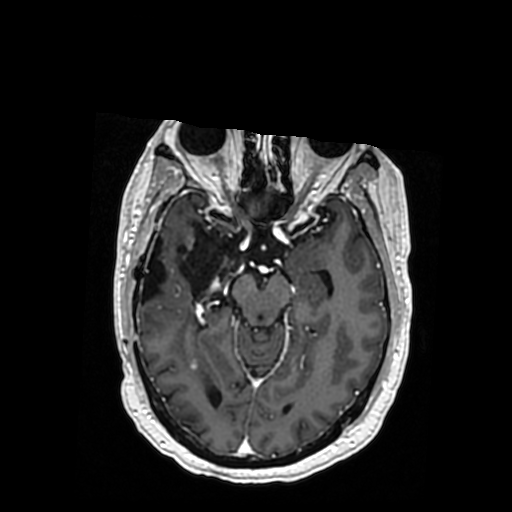
Brain MRI from a brain-tumour surgery series, one axial slice; position 214 of 364 along the scan axis; T1-weighted post-contrast; 0.5 mm slice thickness; 512 × 512 image matrix. From the clinical record (not read from this slice): histopathology: Oligodendroglioma; WHO grade: 3; IDH mutation: yes.
Structures marked on this image (outlined manually by an expert reader):
- previous resection cavity: bounding box <141,225,239,303> (left, top, right, bottom; pixels)